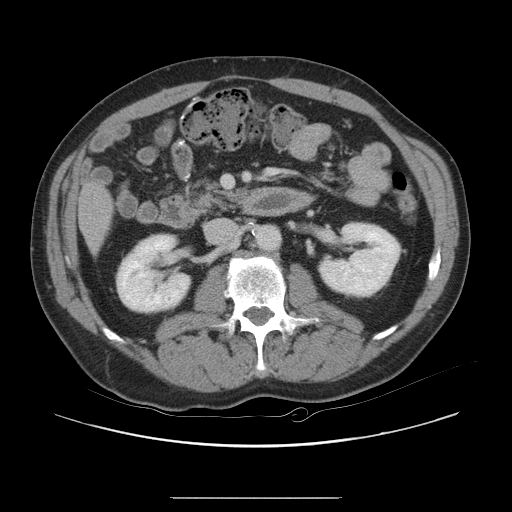
Contrast-enhanced abdominal CT, one axial slice; slice 4 of 40 in the series (ordered by position); intravenous contrast given; soft-tissue window (W 400 / L 40 HU); 5 mm slice thickness; 512 × 512 image matrix, field of view 408 × 408 mm. Male patient, age 64 years. From the clinical record (not read from this slice): diagnosis: colorectal cancer liver metastases, imaged before liver resection; multiple liver metastases: yes; largest metastasis: 3.2 cm.
Outlined on this slice (outlined manually by an expert reader):
- liver: bounding box <81,187,111,248> (left, top, right, bottom; pixels)